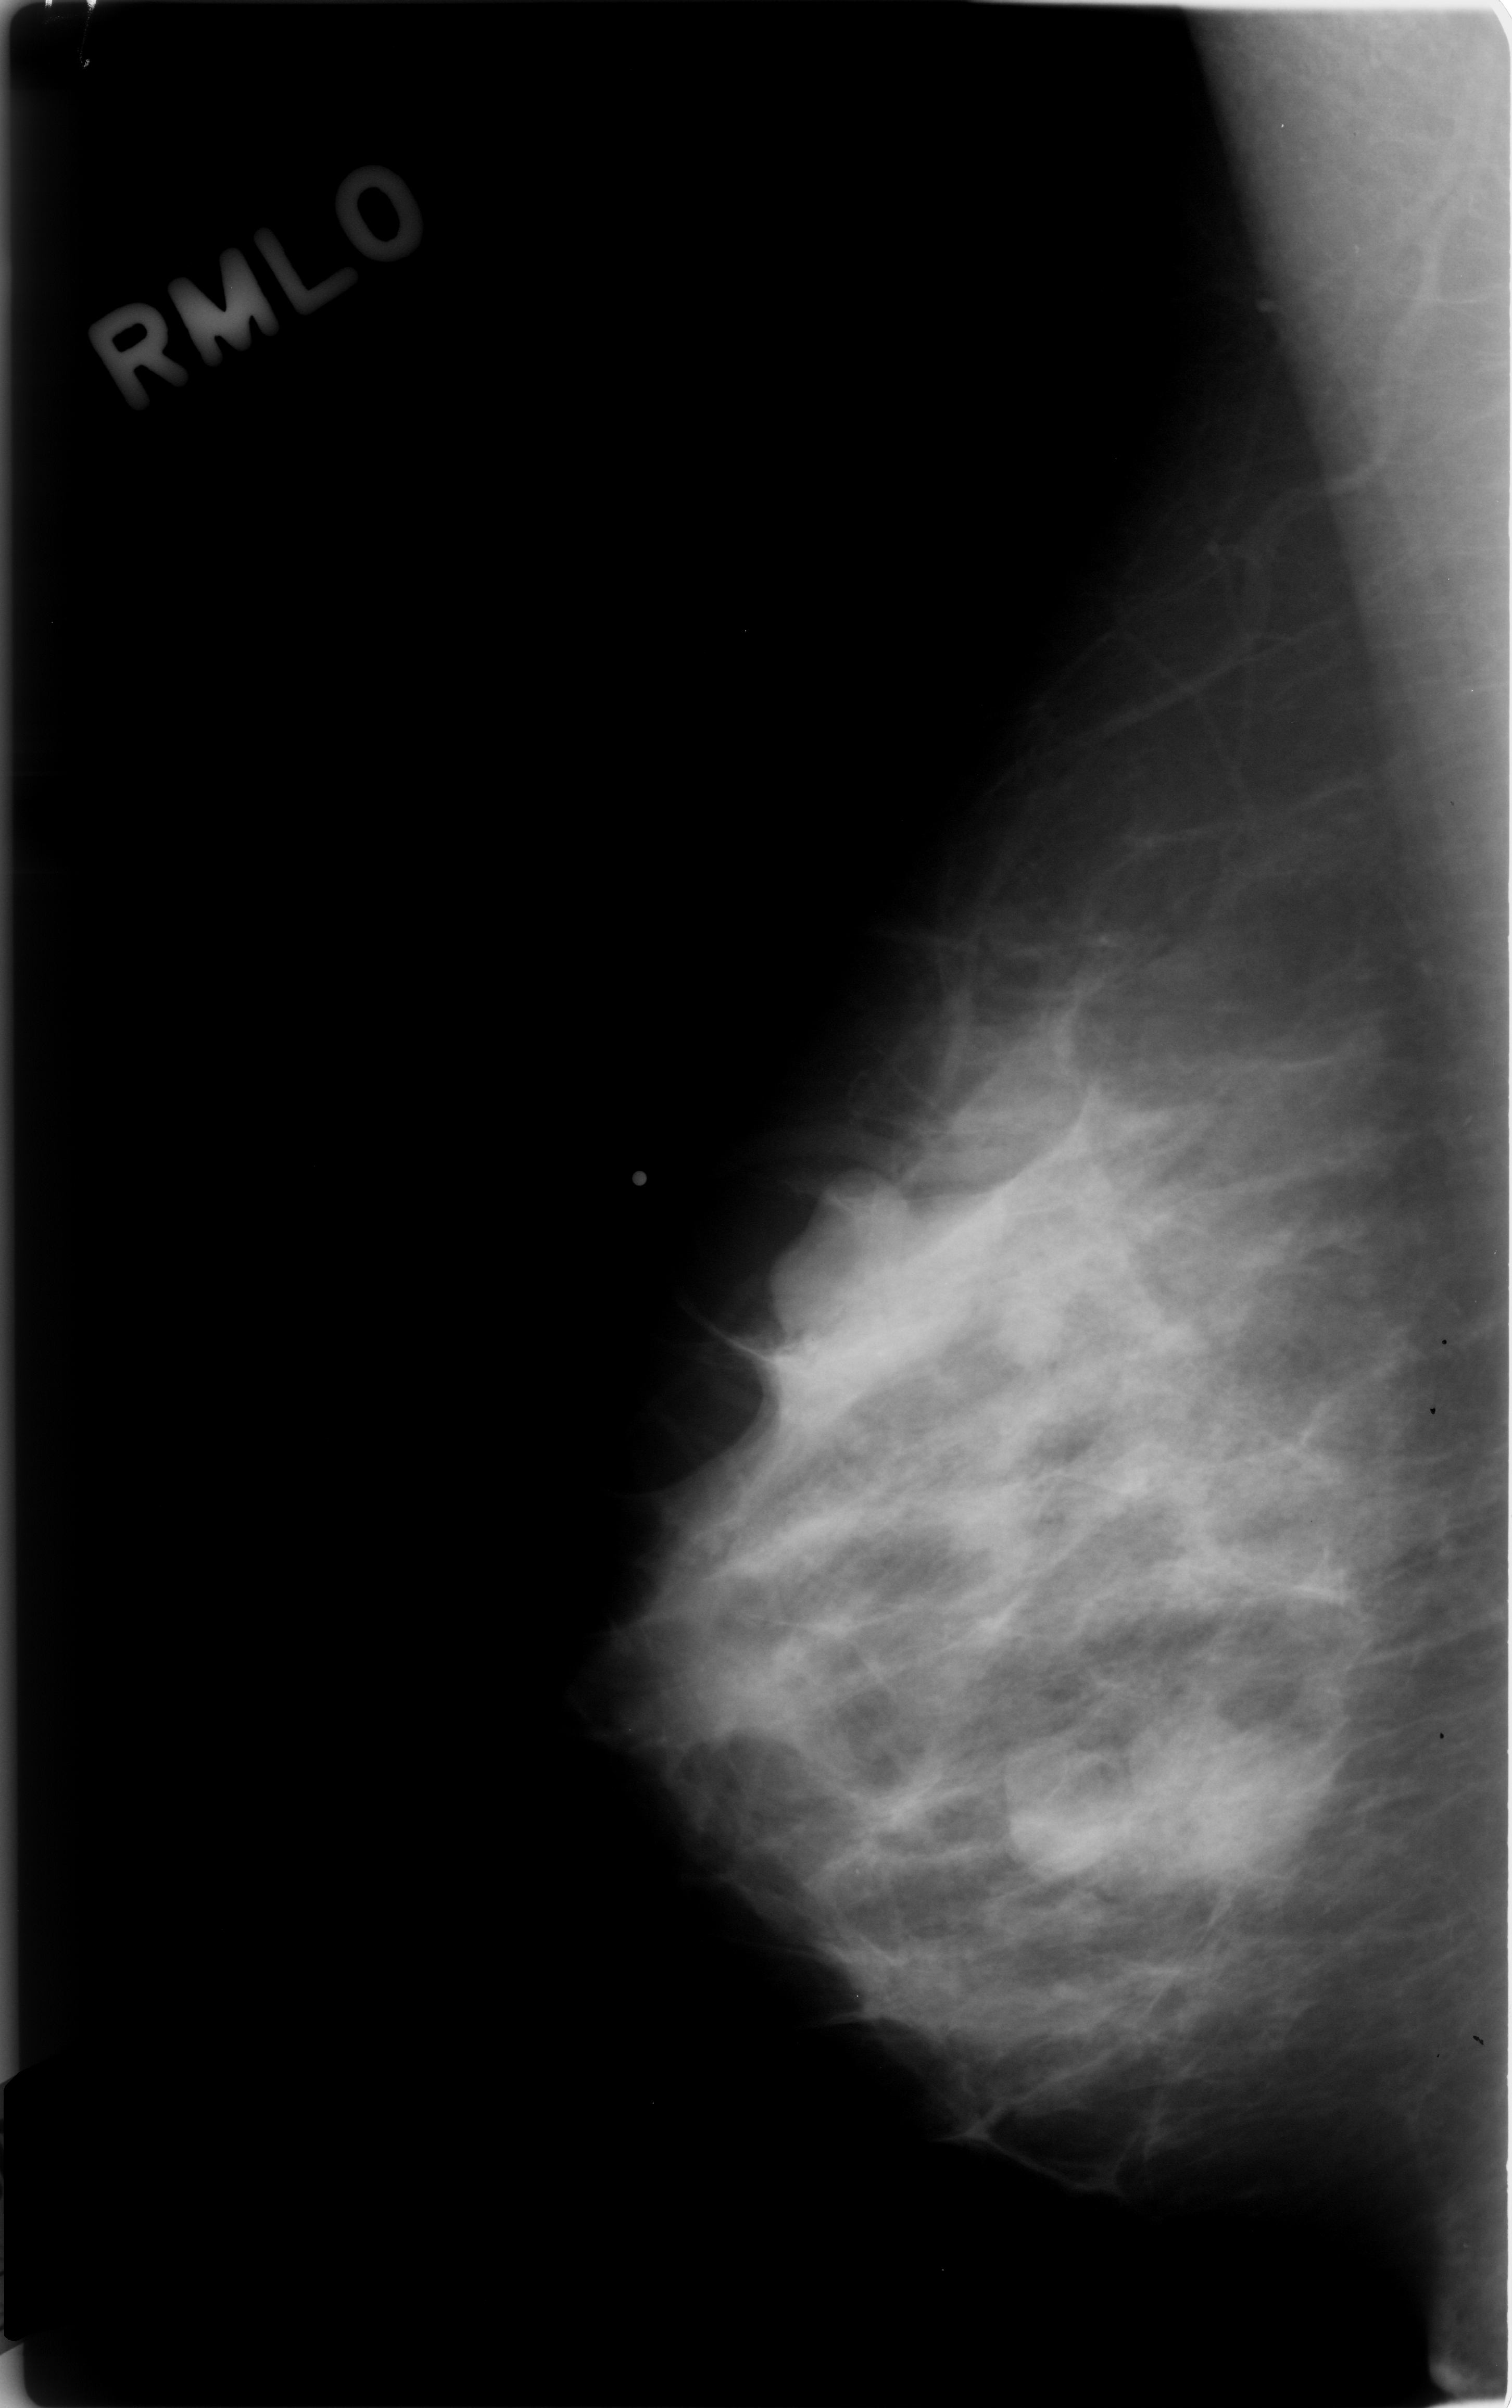
Scanned film-screen mammogram; right breast; mediolateral oblique (MLO) view; BI-RADS breast density category 3 (scale 1–4).
Mass, shape lobulated, margins obscured; BI-RADS assessment category 4; pathology result (as recorded, not read from the image): benign.